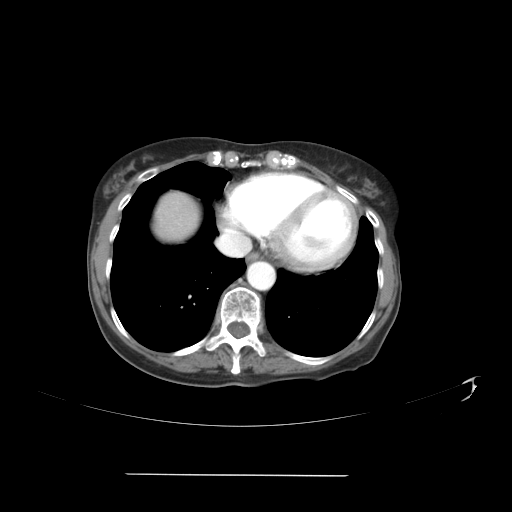
Contrast-enhanced abdominal CT, one axial slice; position 38 of 41 along the scan axis; 120 kVp; intravenous contrast given; soft-tissue window (W 400 / L 40 HU); 5 mm slice thickness; 512 × 512 image matrix, field of view 431 × 431 mm. Female patient, age 74 years. From the clinical record (not read from this slice): diagnosis: colorectal cancer liver metastases, imaged before liver resection; multiple liver metastases: yes; largest metastasis: 3.3 cm; chemotherapy before resection: yes.
Annotated regions visible in this slice (expert manual segmentation):
- liver: bounding box [x1, y1, x2, y2] px = [156, 194, 197, 239]
- planned liver remnant (the part of the liver to remain after resection): [156, 194, 197, 237]